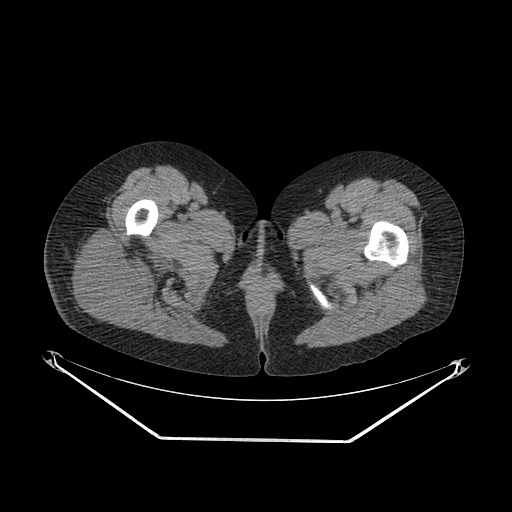
CT of an extremity soft-tissue mass (from a PET/CT study), one axial slice; slice 30 of 267 in the series (ordered by position); reconstruction kernel SOFT; soft-tissue window (W 400 / L 40 HU); 3.75 mm slice thickness; 512 × 512 image matrix, field of view 500 × 500 mm. Female patient. Case-level facts recorded for this patient, not image findings: histological type: epithelioid sarcoma with vascular differentiation; site of the primary tumour: right buttock.
Annotated regions visible in this slice (expert contour drawn on MRI and transferred to this co-registered scan by the dataset authors):
- gross tumour volume (mass): box from (x=71, y=233) to (x=149, y=318) px